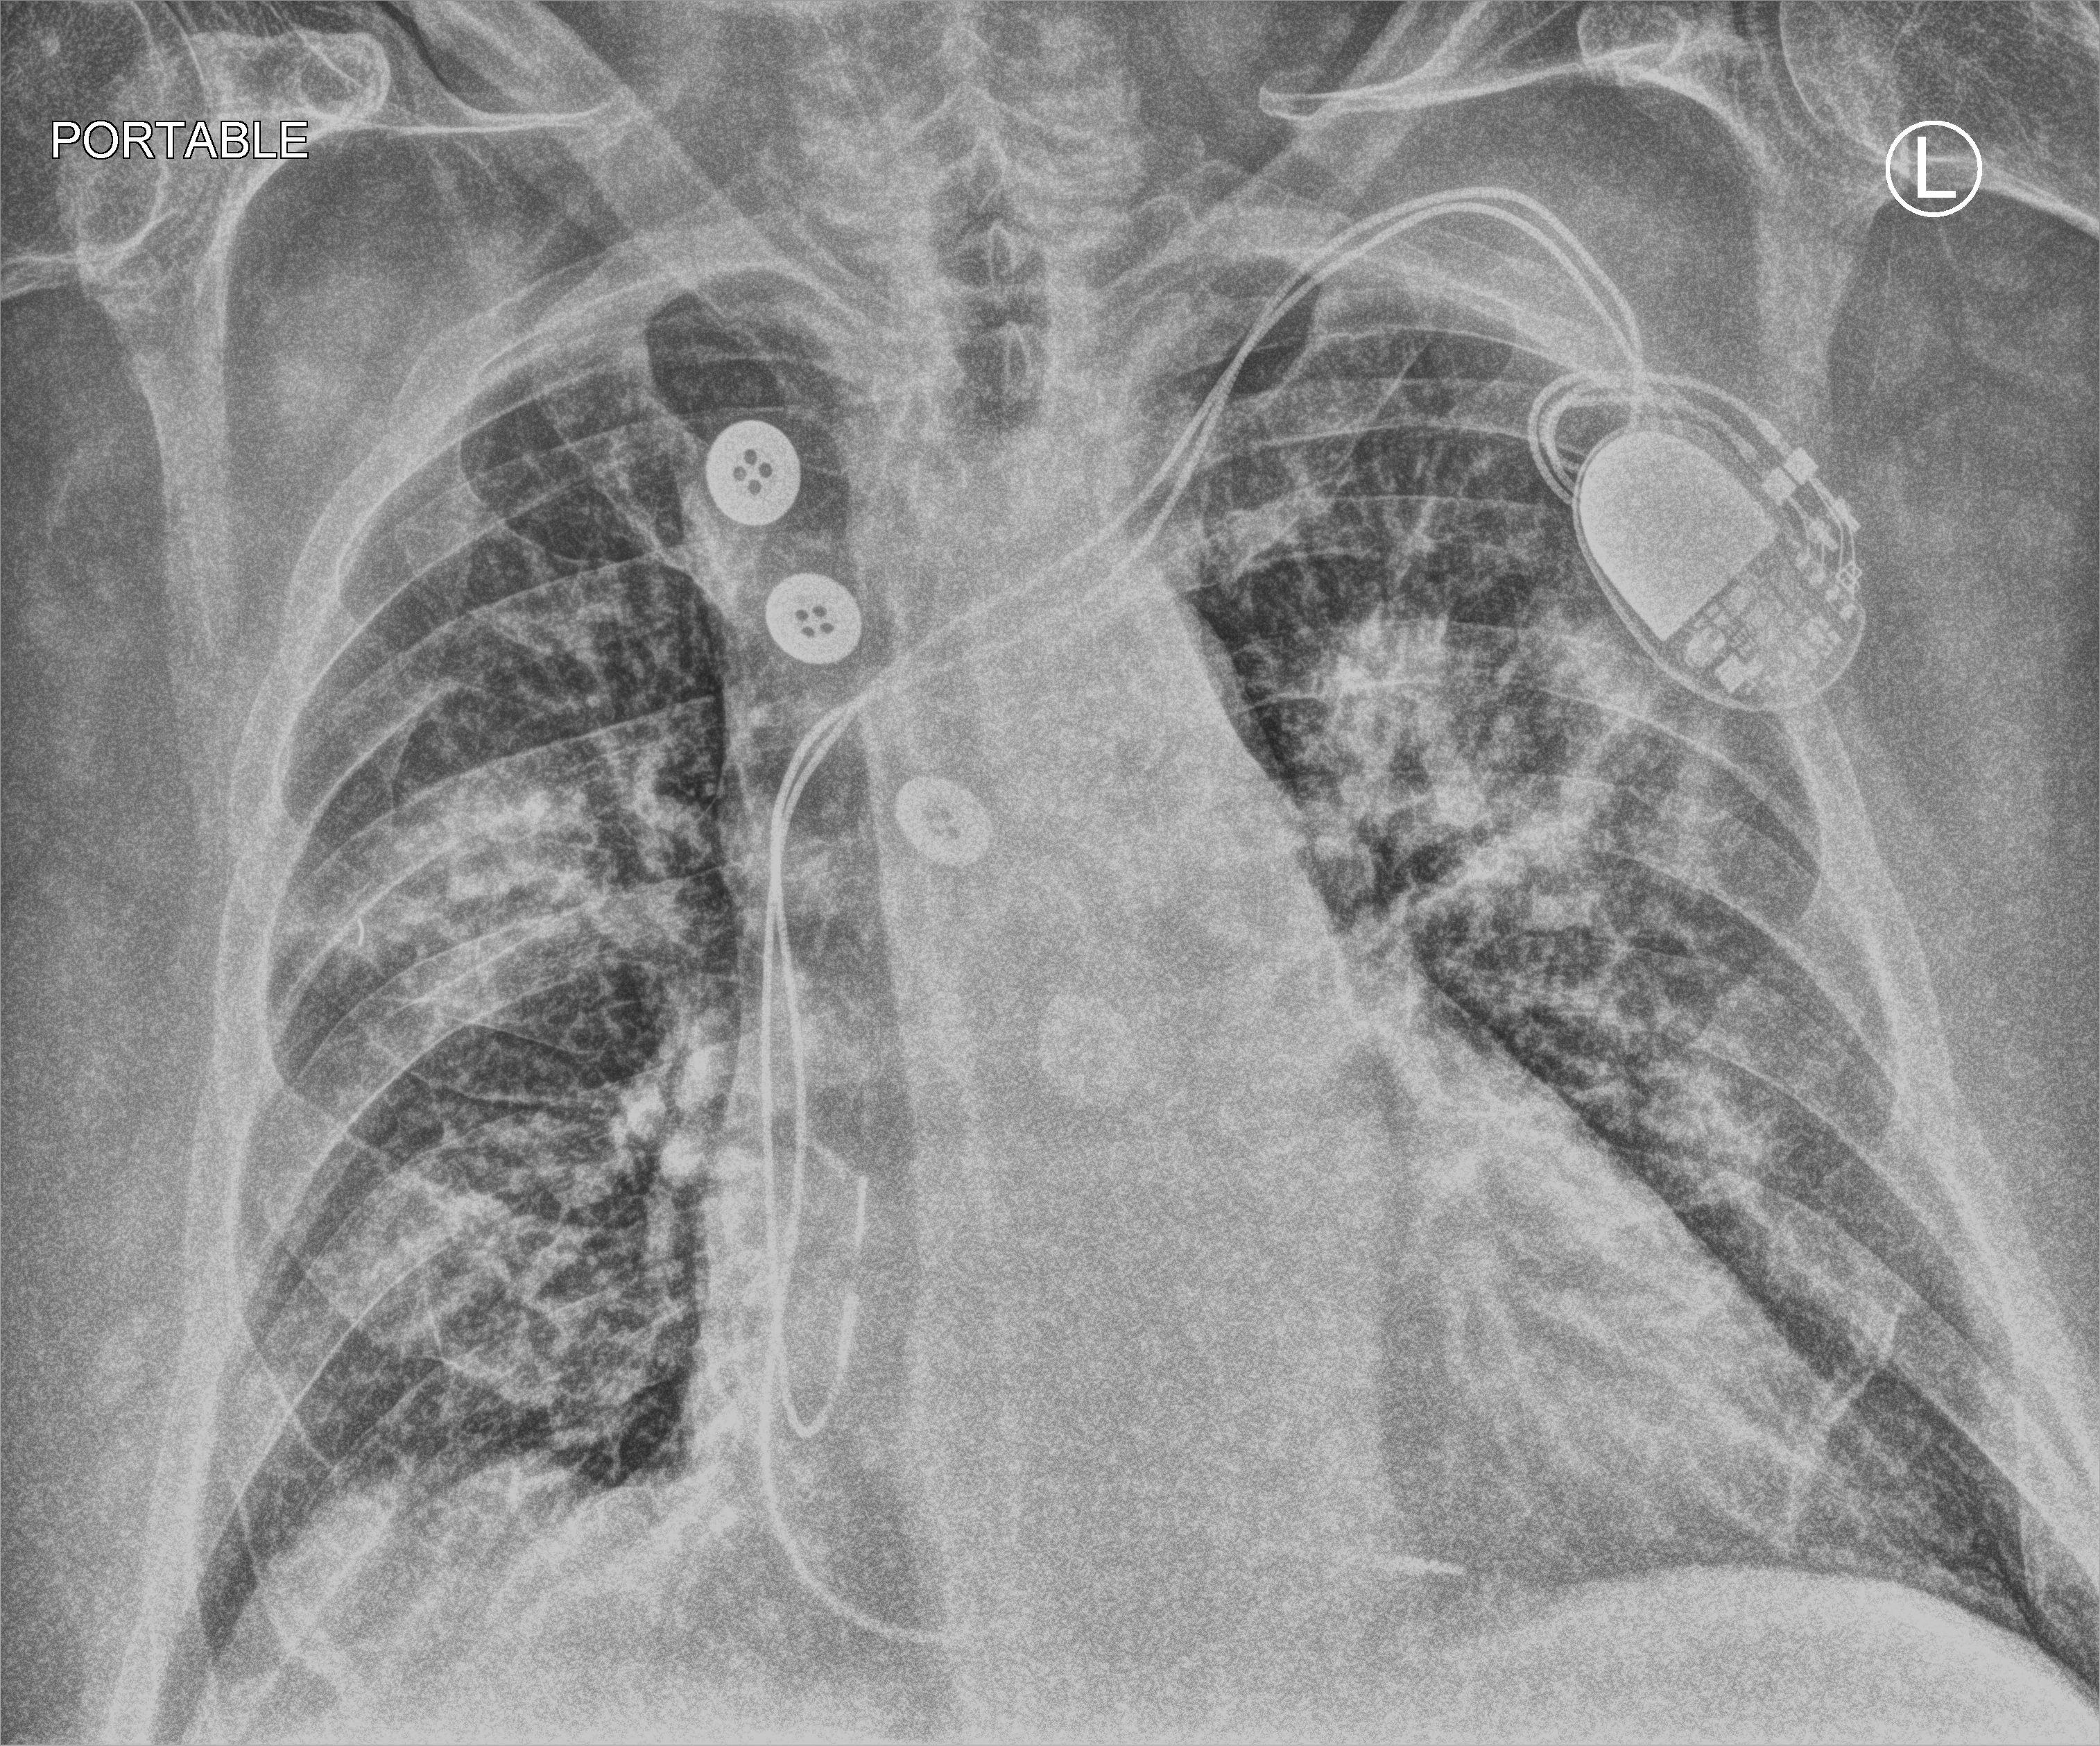
Chest X-ray (portable). Patient hospitalised with COVID-19; male, aged 75–90 years.
From the hospital-stay record, not from the radiograph (when in the stay this image was taken is not recorded): chronic kidney disease (admission record): no; admitted to intensive care during this hospital stay: no; mechanically ventilated during this hospital stay: no.